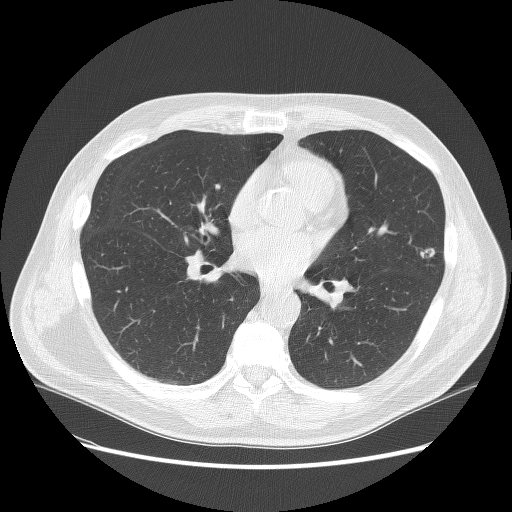
Low-dose screening chest CT, axial slice. Second screening round (one year after baseline). Lung window (W 1500 / L -600 HU). 2.5 mm slice thickness. 120 kVp. Slice 63 of 138 in the series. Male participant, aged 67 years at enrolment.
Lesion marked by an expert reader, bounding box <401,234,454,280> (left, top, right, bottom; pixels). Screening reader's record for this exam (one nodule recorded; not confirmed to be the boxed lesion): non-calcified nodule or mass ≥4 mm, left upper lobe, 10 × 6 mm, soft tissue attenuation, pre-existing on the prior screen: yes; interval growth: no. Official screen result: positive, no significant change: stable abnormalities potentially related to lung cancer, unchanged since the prior screening exam. Participant outcome: lung cancer diagnosed 393 days after this screen — squamous cell carcinoma, NOS, left upper lobe, moderately differentiated (G2), stage IB (AJCC 6th edition), 25 mm at pathology.